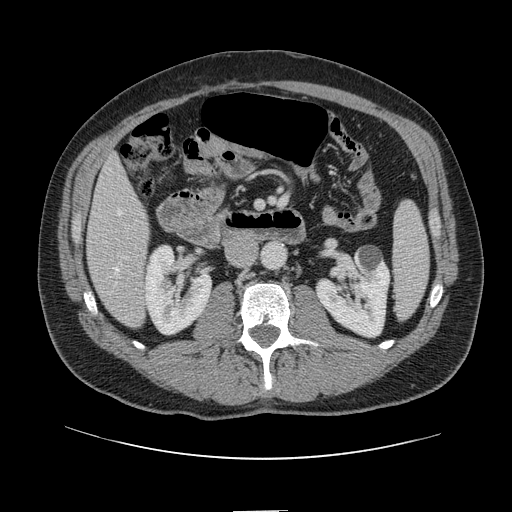
Contrast-enhanced abdominal CT, one axial slice; position 36 of 161 along the scan axis; soft-tissue window (W 400 / L 40 HU); 2.5 mm slice thickness; 512 × 512 image matrix, field of view 412 × 412 mm. Male patient, age 66 years. From the clinical record (not read from this slice): diagnosis: colorectal cancer liver metastases, imaged before liver resection; multiple liver metastases: no; largest metastasis: 3.5 cm.
Structures marked on this image (outlined manually by an expert reader):
- hepatic veins: bounding box <115,210,122,275> (left, top, right, bottom; pixels)
- liver: <87,159,149,326>
- planned liver remnant (the part of the liver to remain after resection): <87,159,147,266>